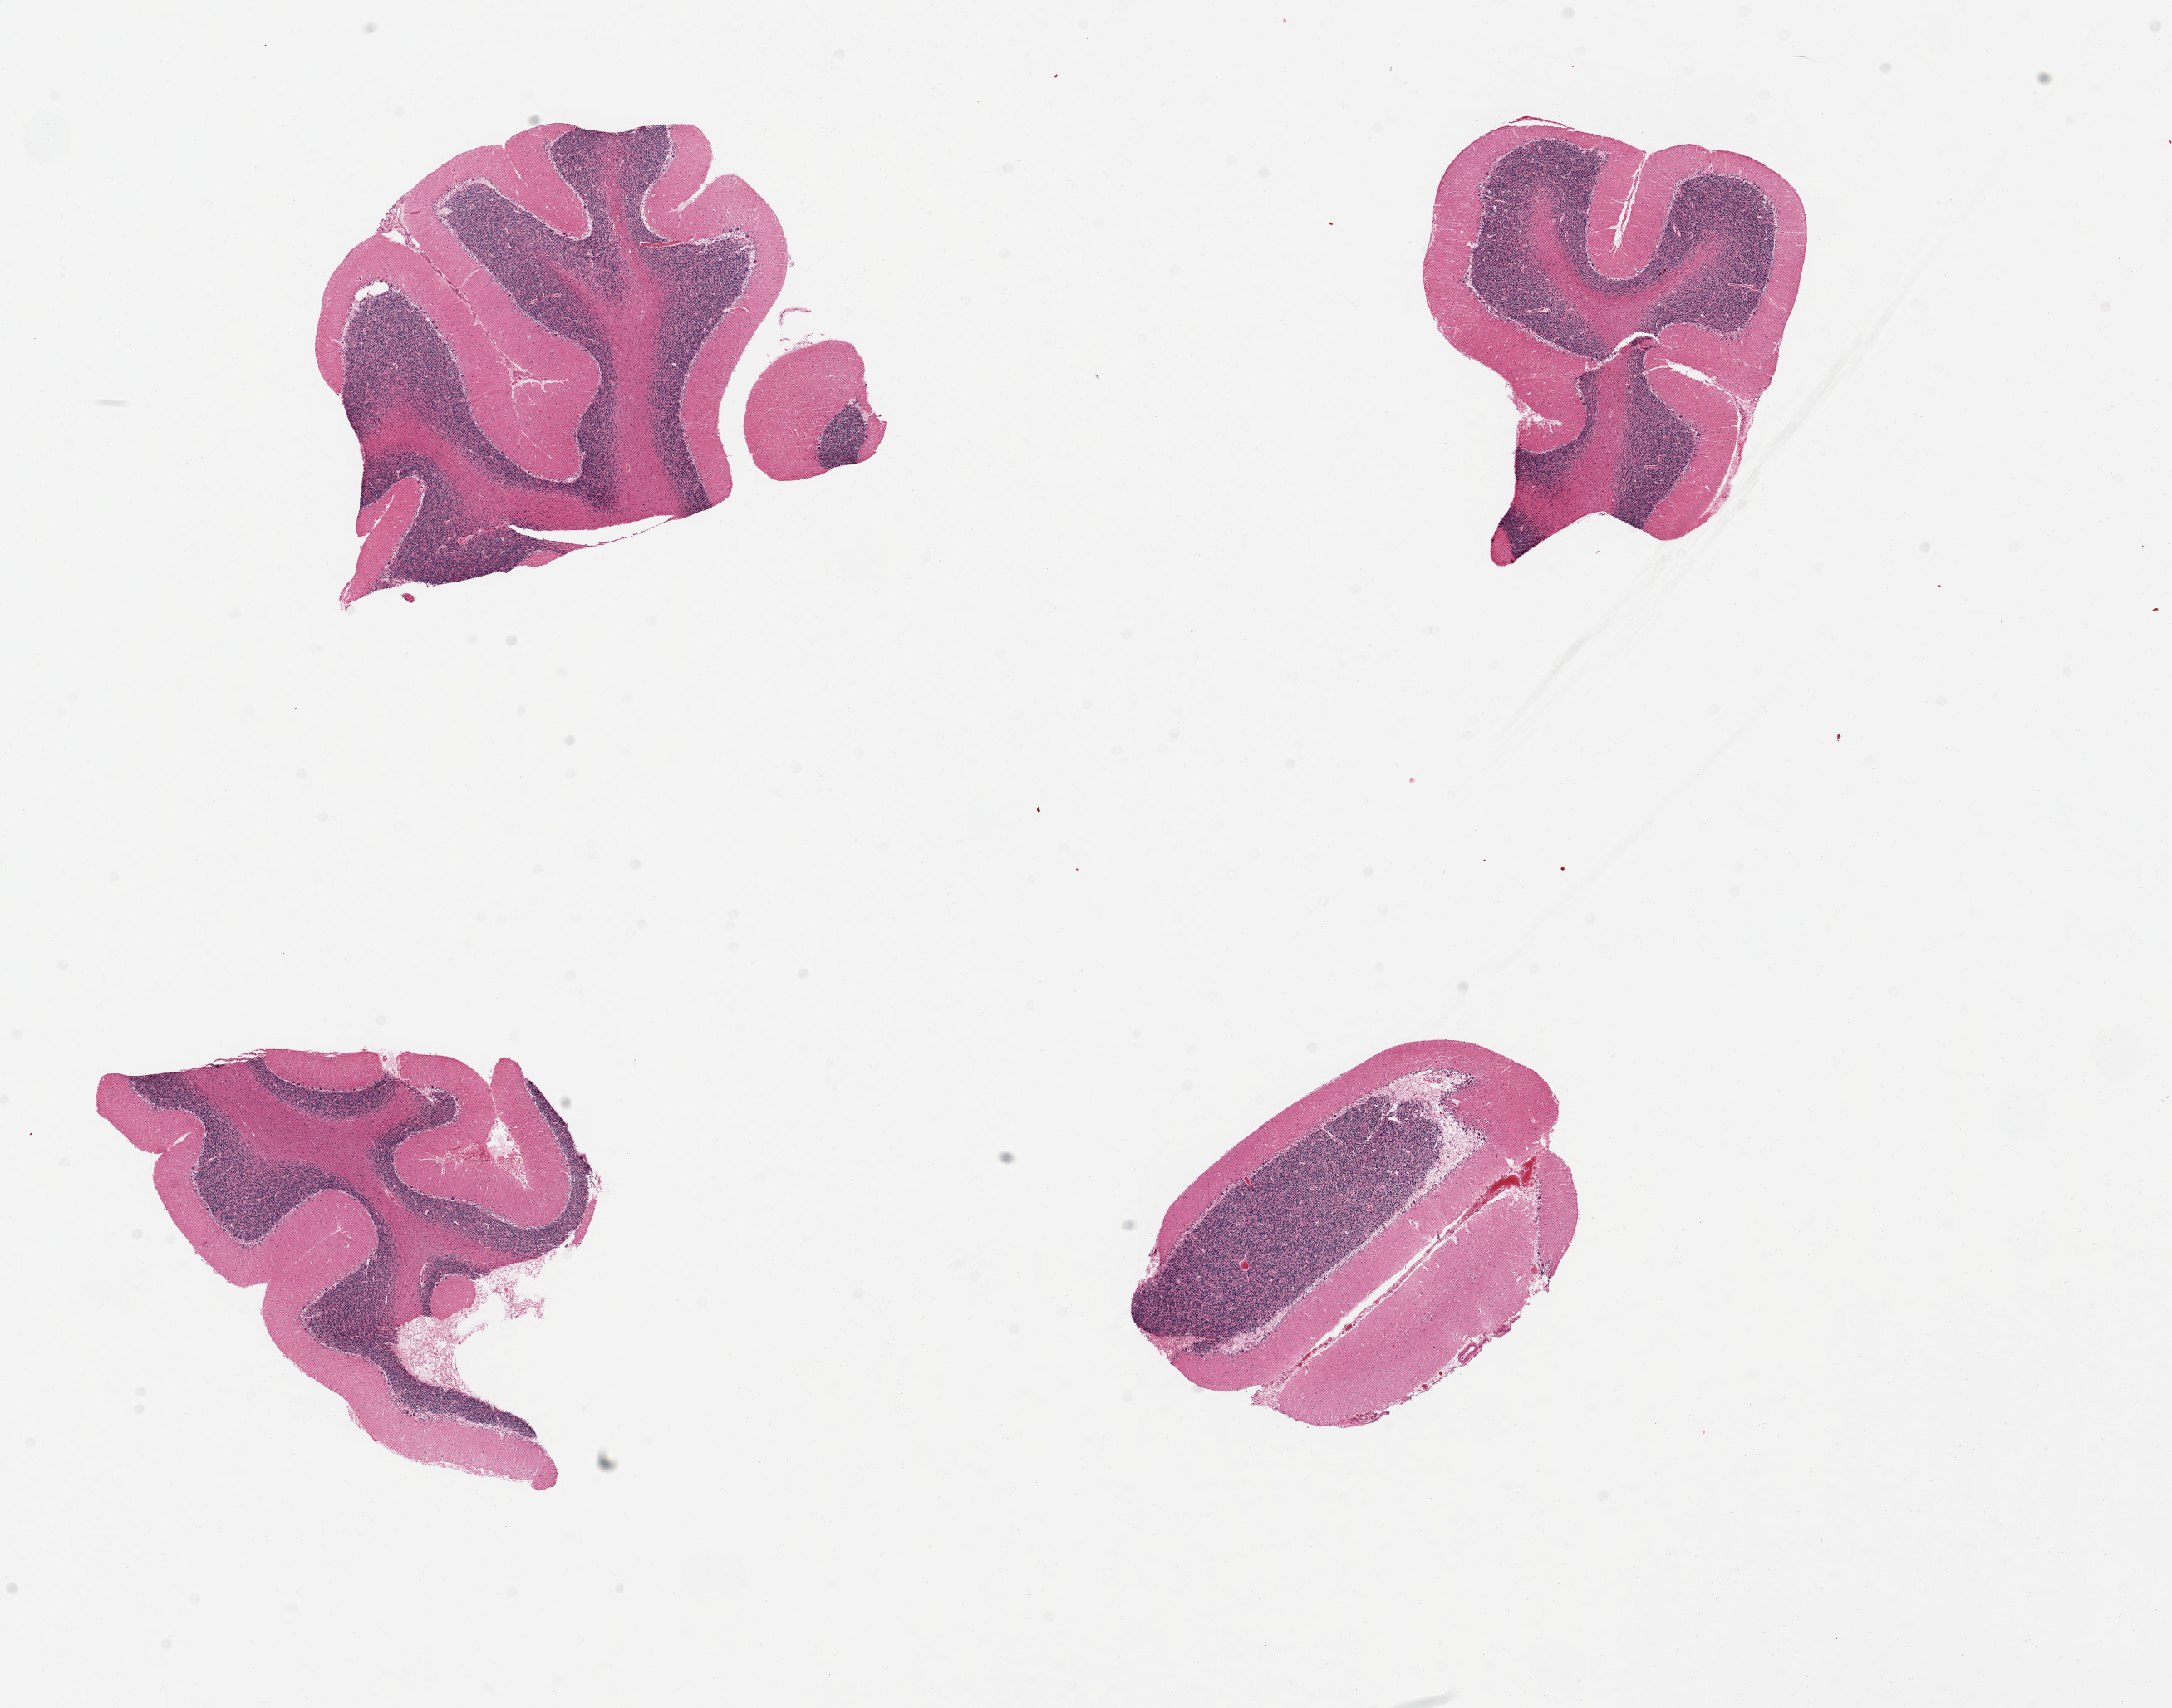
Digitized haematoxylin and eosin-stained section, whole scanned area (about 20.7 x 16.3 mm) shown as a low-resolution overview. PAXgene-fixed, paraffin-embedded tissue. Sampled site (target tissue): cerebellum. Donor tissue sample.
Pathologist's review note for this sample: 4 pieces, no abnormalities.